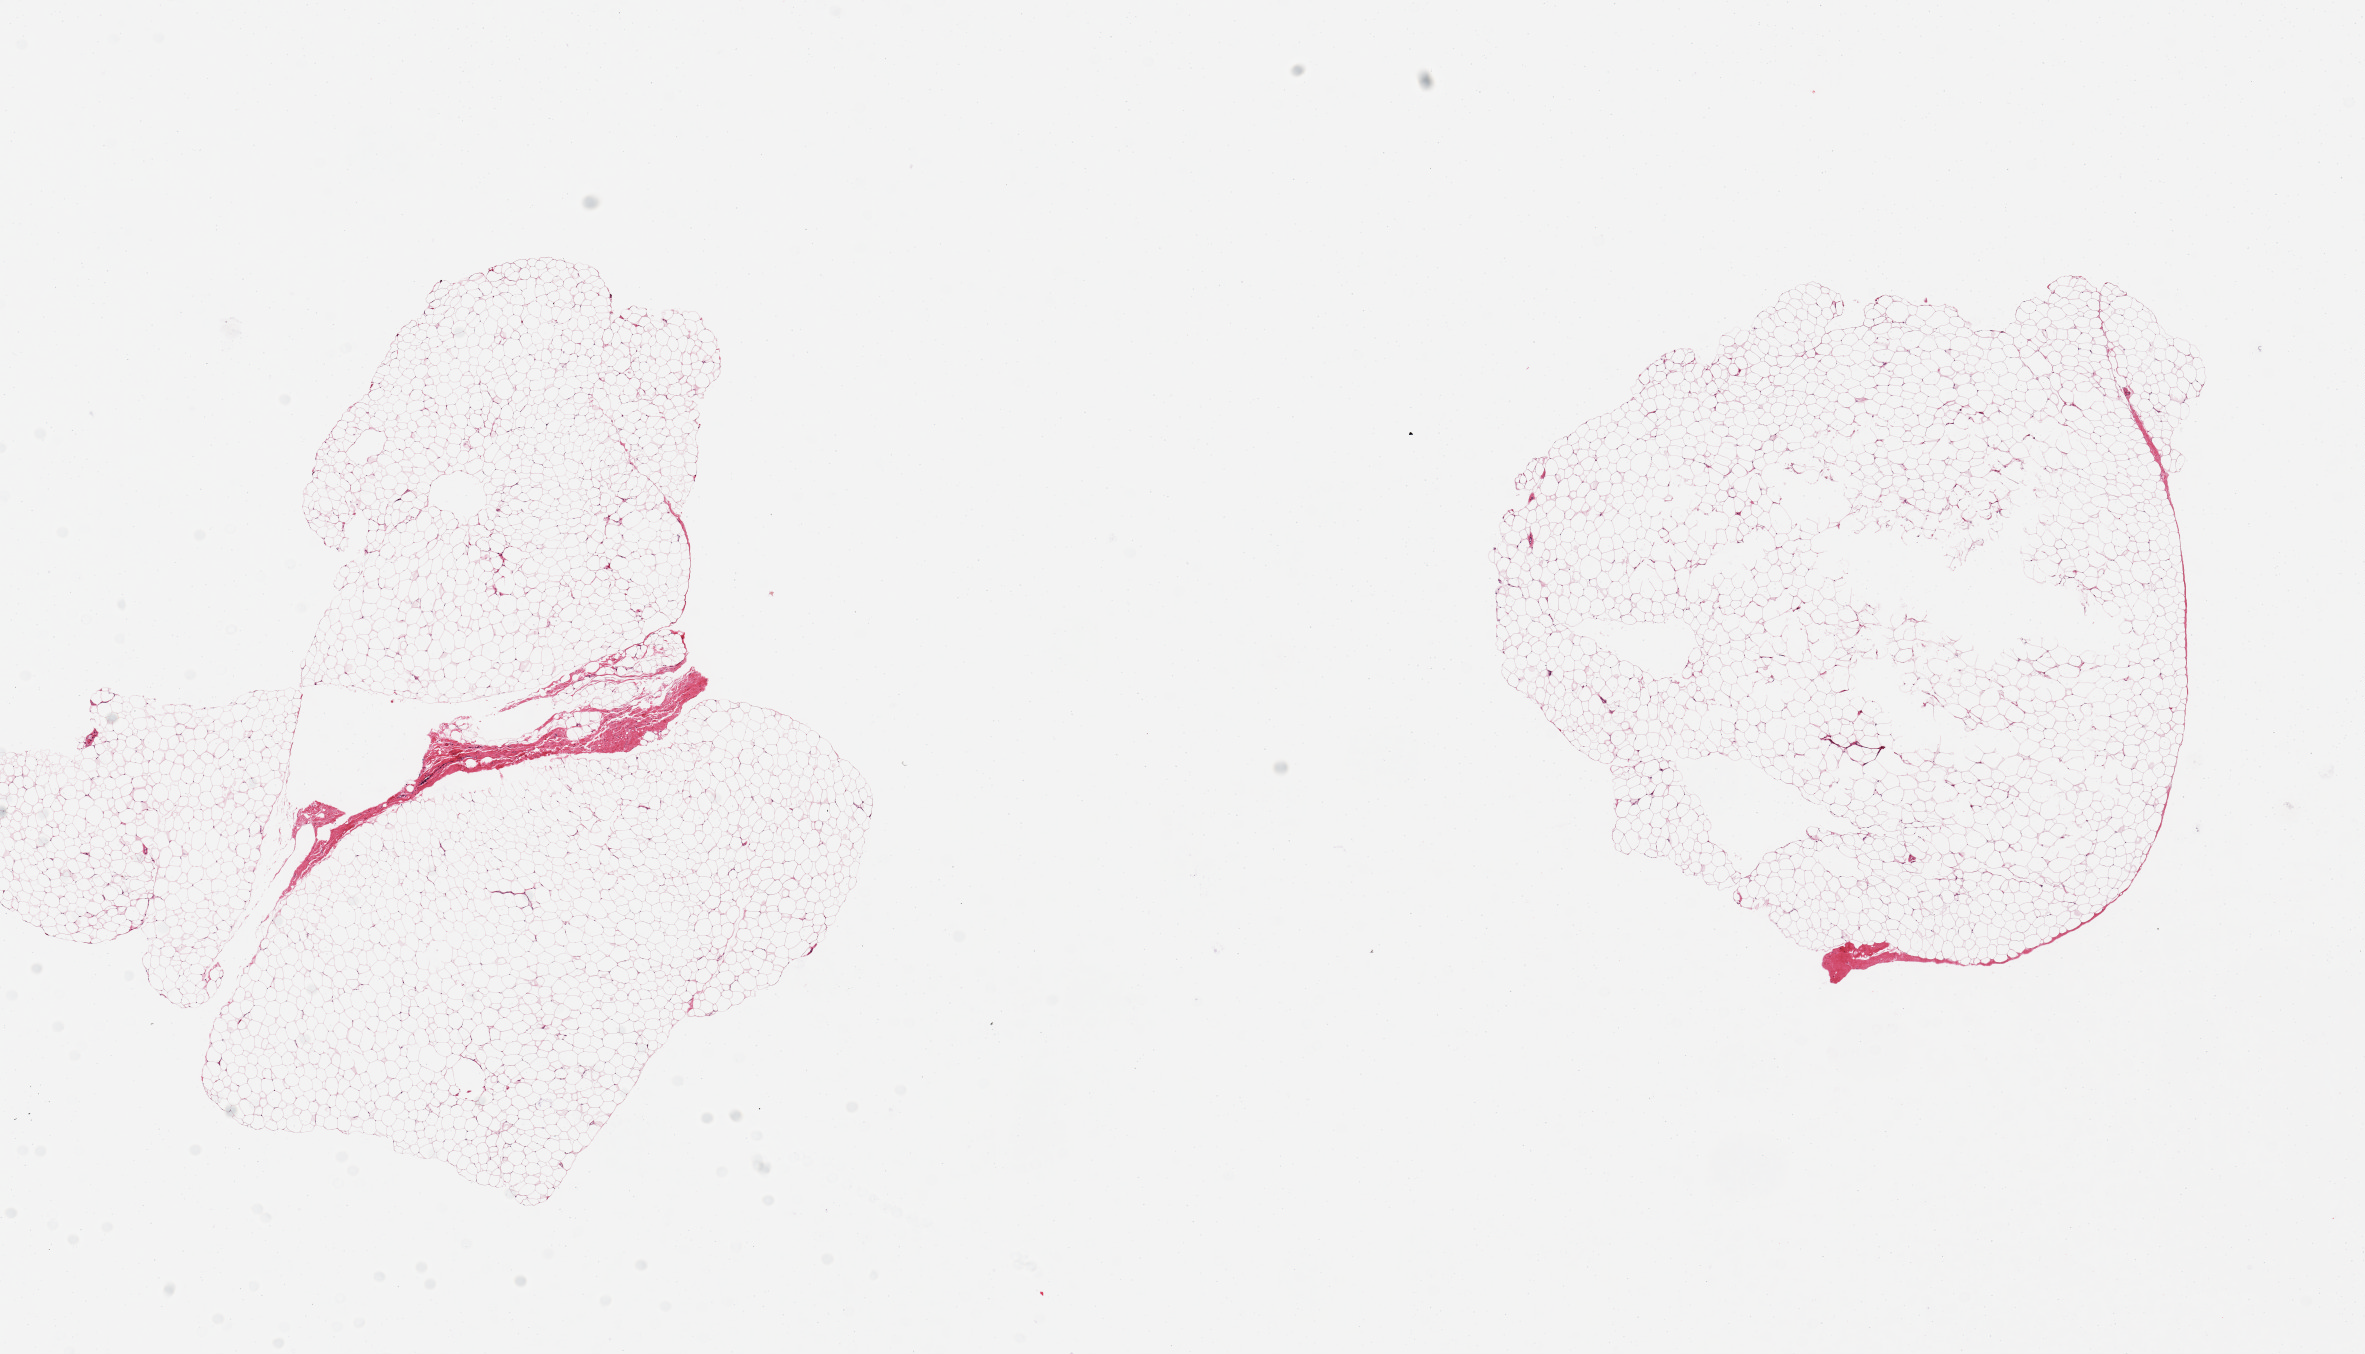
Digitized haematoxylin and eosin-stained section, low-resolution overview of the scanned area, about 18.7 x 10.7 mm; PAXgene-fixed paraffin-embedded (PFPE) section; sampled site (target tissue): breast; tissue donor sample.
Review note (as recorded): 2 aliquots, ~6x6mm. No mammary ductal elements noted.